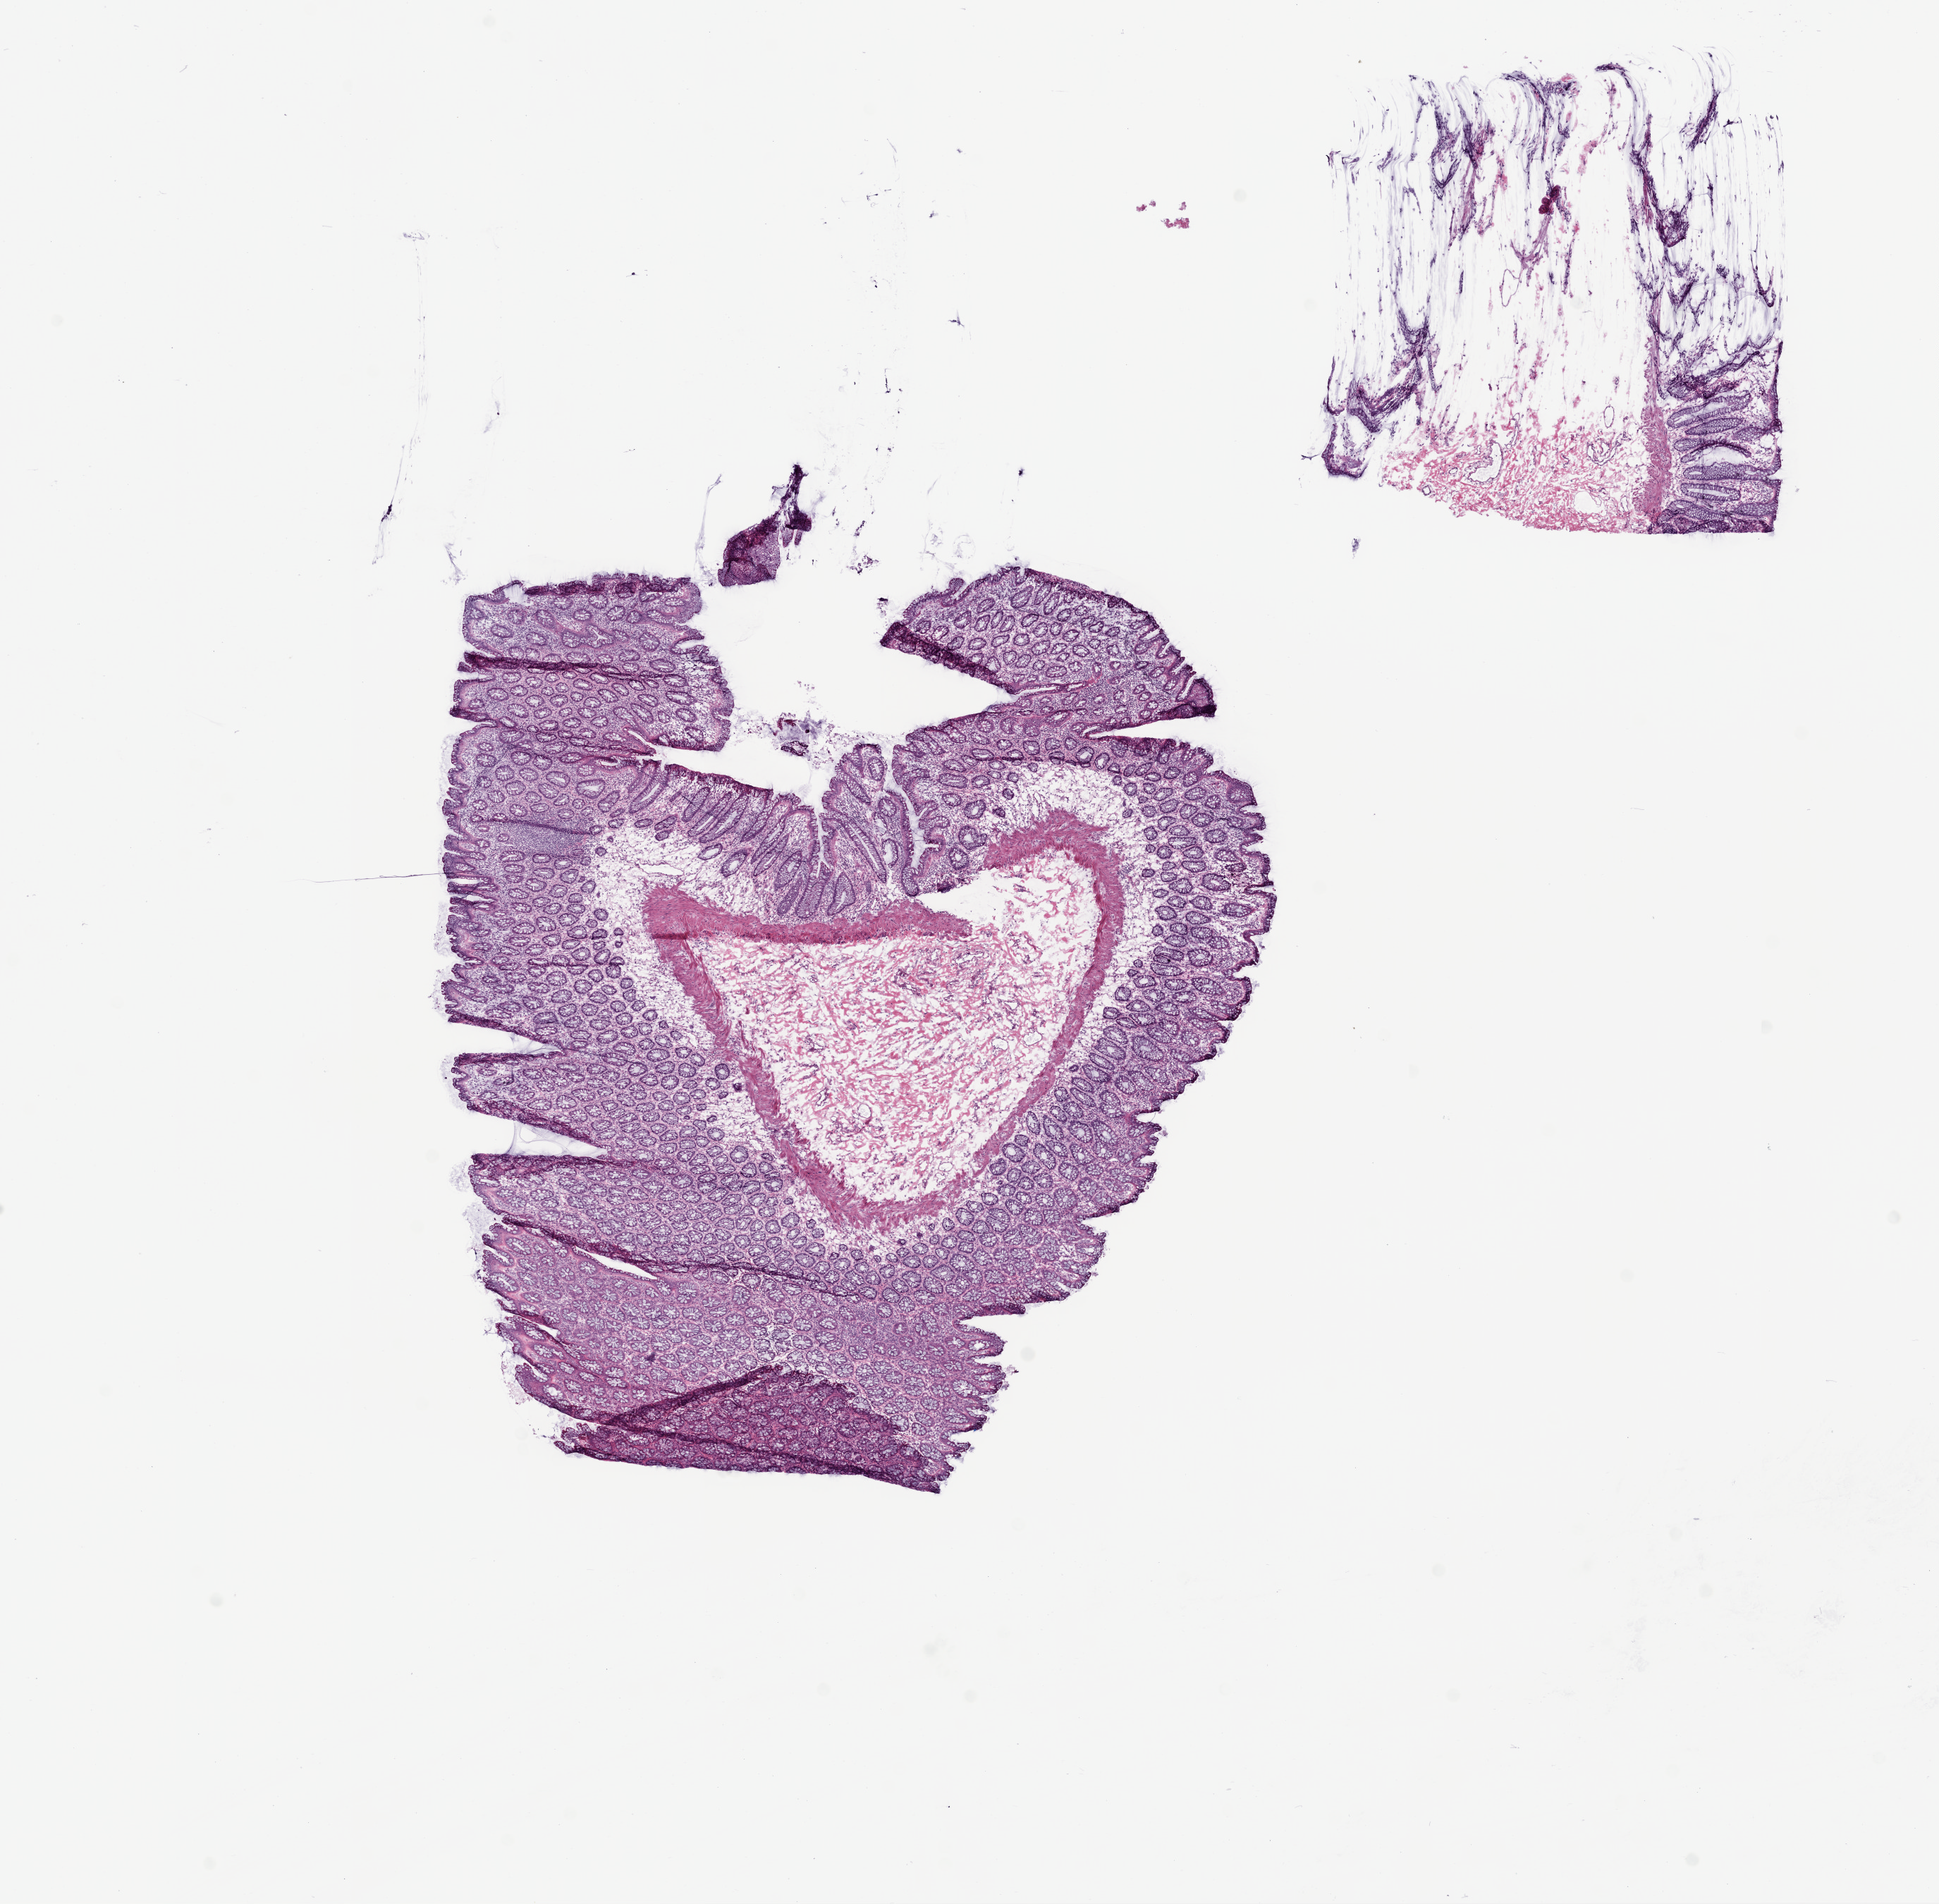
Digitized Hematoxylin and eosin (H&E) stained tissue section (whole slide), low-resolution overview of the scanned area, about 11.0 x 10.8 mm (slide scanned at 20x), frozen section from the top of the tissue portion, colon, solid tissue normal (non-tumour tissue) sample. Female, age 51 years at initial diagnosis.
This section: solid tissue normal sample (biorepository sample class). Patient diagnosis: Adenocarcinoma, NOS.